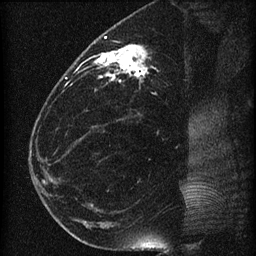
Breast MRI (dynamic contrast-enhanced), one sagittal slice; slice 28 of 60 in the series (ordered by position); dynamic contrast-enhanced series, image 2 of 4 at this slice position (ordered by acquisition); 1.5 T; TE 4.2 ms, TR 22.7 ms; 1.5 mm slice thickness; 256 × 256 image matrix, field of view 180 × 180 mm. Patient: female, 35 years. Case-level facts recorded for this patient, not image findings: setting: breast cancer imaged before/during neoadjuvant chemotherapy; receptor status: HR-positive, HER2-negative.
Outlined on this slice (semi-automatic segmentation, software-assisted and operator-edited):
- analysis volume of interest (the breast-tissue region the enhancement analysis was run in; not a lesion): bounding box (x1, y1, x2, y2) in pixels: (69, 27, 198, 112)
- tumour enhancement mask (voxels above the 90 % enhancement threshold inside the analysis volume of interest): (93, 37, 148, 80)